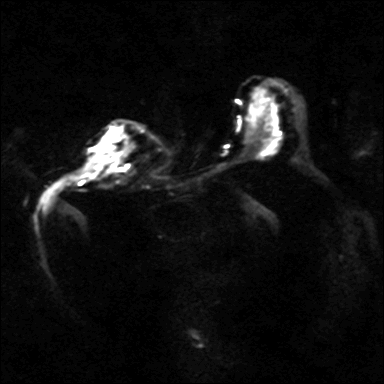
Breast MRI, one axial slice. Position 24 of 40 along the scan axis. Diffusion-weighted series; image 2 of 4 stored at this slice position (different b-values; order by instance number). 3 T. 4.2 mm slice thickness. 384 × 384 image matrix, field of view 320 × 320 mm. Female patient.
Structures marked on this image (expert manual segmentation):
- tumour on diffusion-weighted imaging: bounding box [x1, y1, x2, y2] px = [92, 143, 112, 178]